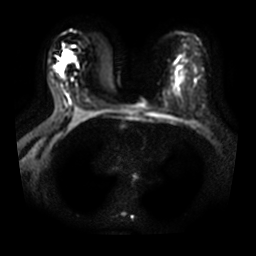
Breast MRI, one axial slice. Position 21 of 33 along the scan axis. Diffusion-weighted series; image 2 of 4 stored at this slice position (different b-values; order by instance number). 3 T. 256 × 256 image matrix, field of view 350 × 350 mm. Female patient.
Structures marked on this image (expert manual segmentation):
- tumour on diffusion-weighted imaging: bounding box <64,51,66,57> (left, top, right, bottom; pixels)